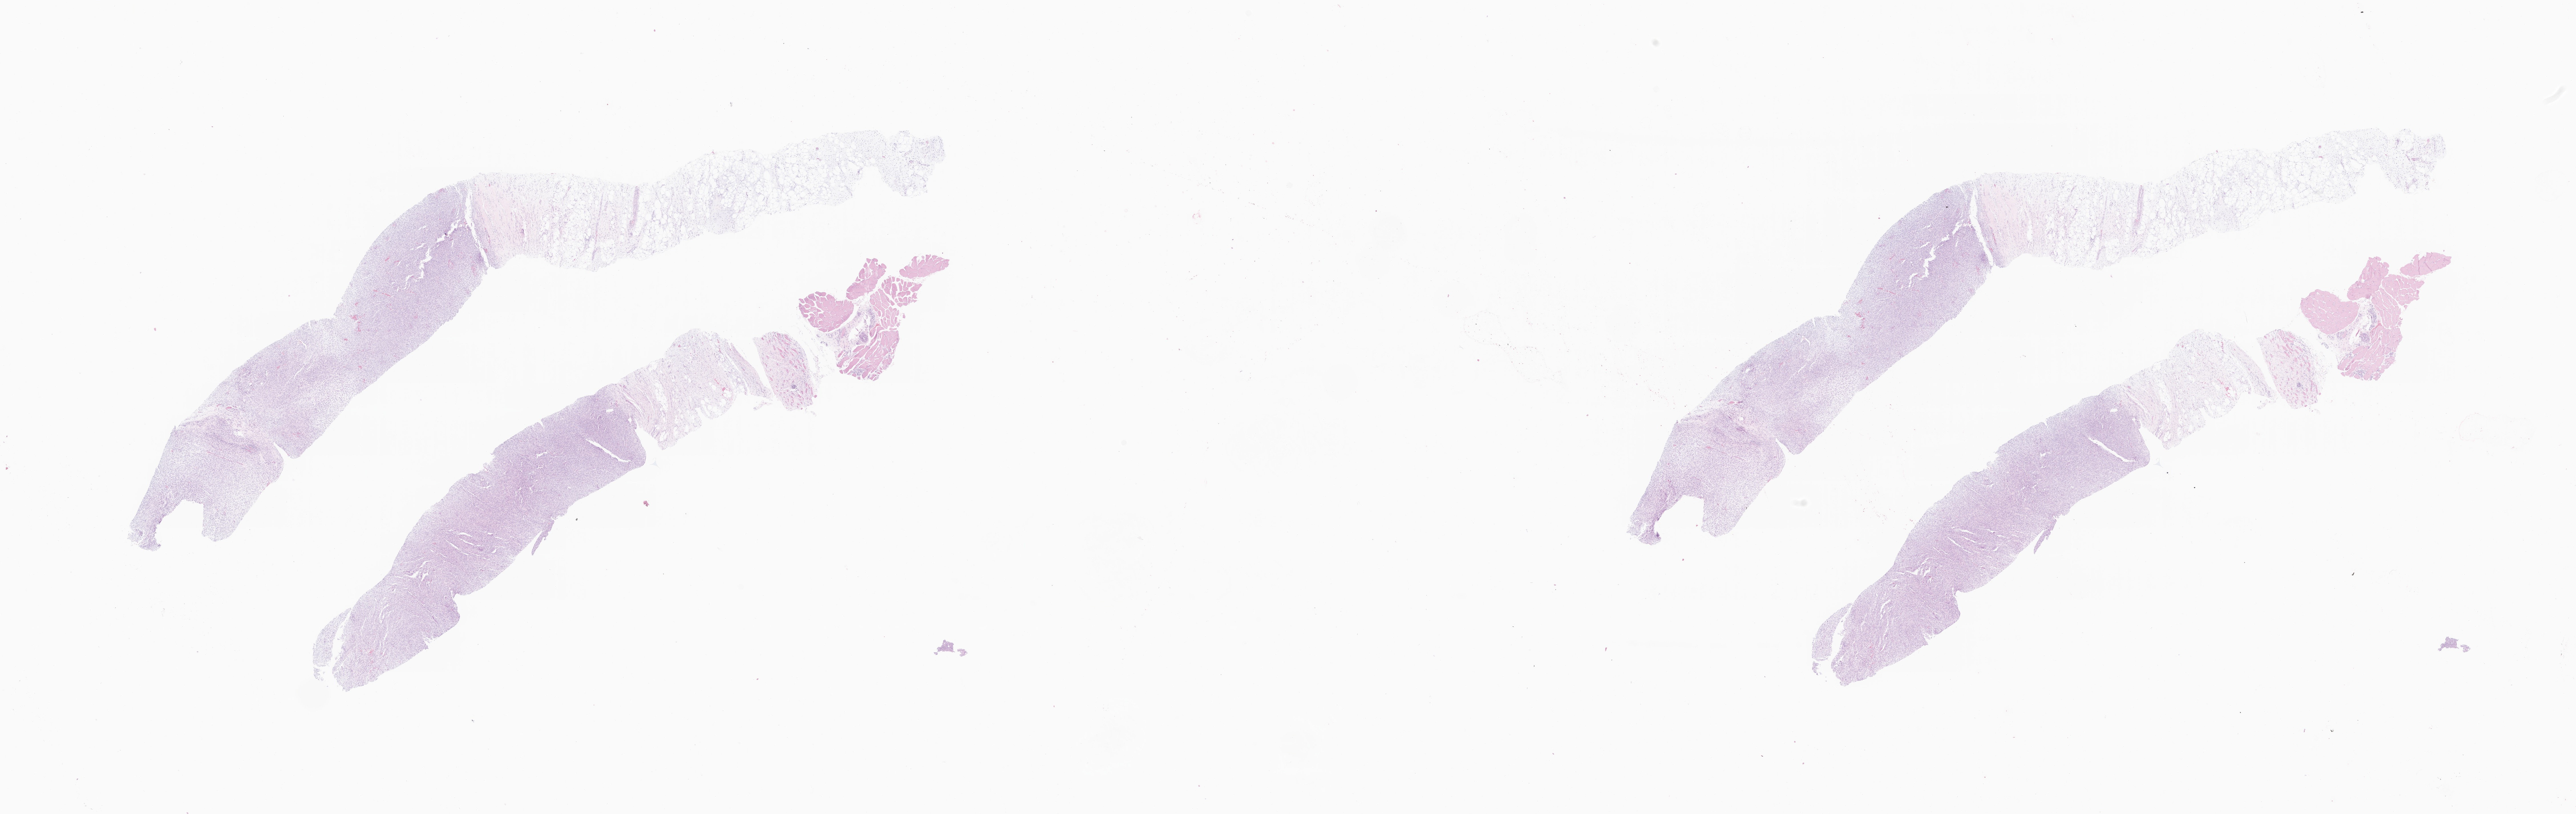
Digitized hematoxylin and eosin (H&E)-stained section of tumor tissue from the upper limb, low-resolution overview of the scanned area, about 38.1 x 12.0 mm. Formalin-fixed, paraffin-embedded (FFPE) tissue. Patient male; age 248 months (20 years 8 months).
Diagnosis: Spindle cell sarcoma.